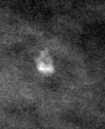
Region of interest cut from a scanned film mammogram (one marked finding); left breast; MLO view.
Marked abnormality: calcifications, morphology lucent center; BI-RADS assessment category 2; benign; no additional work-up was recommended (benign without callback).